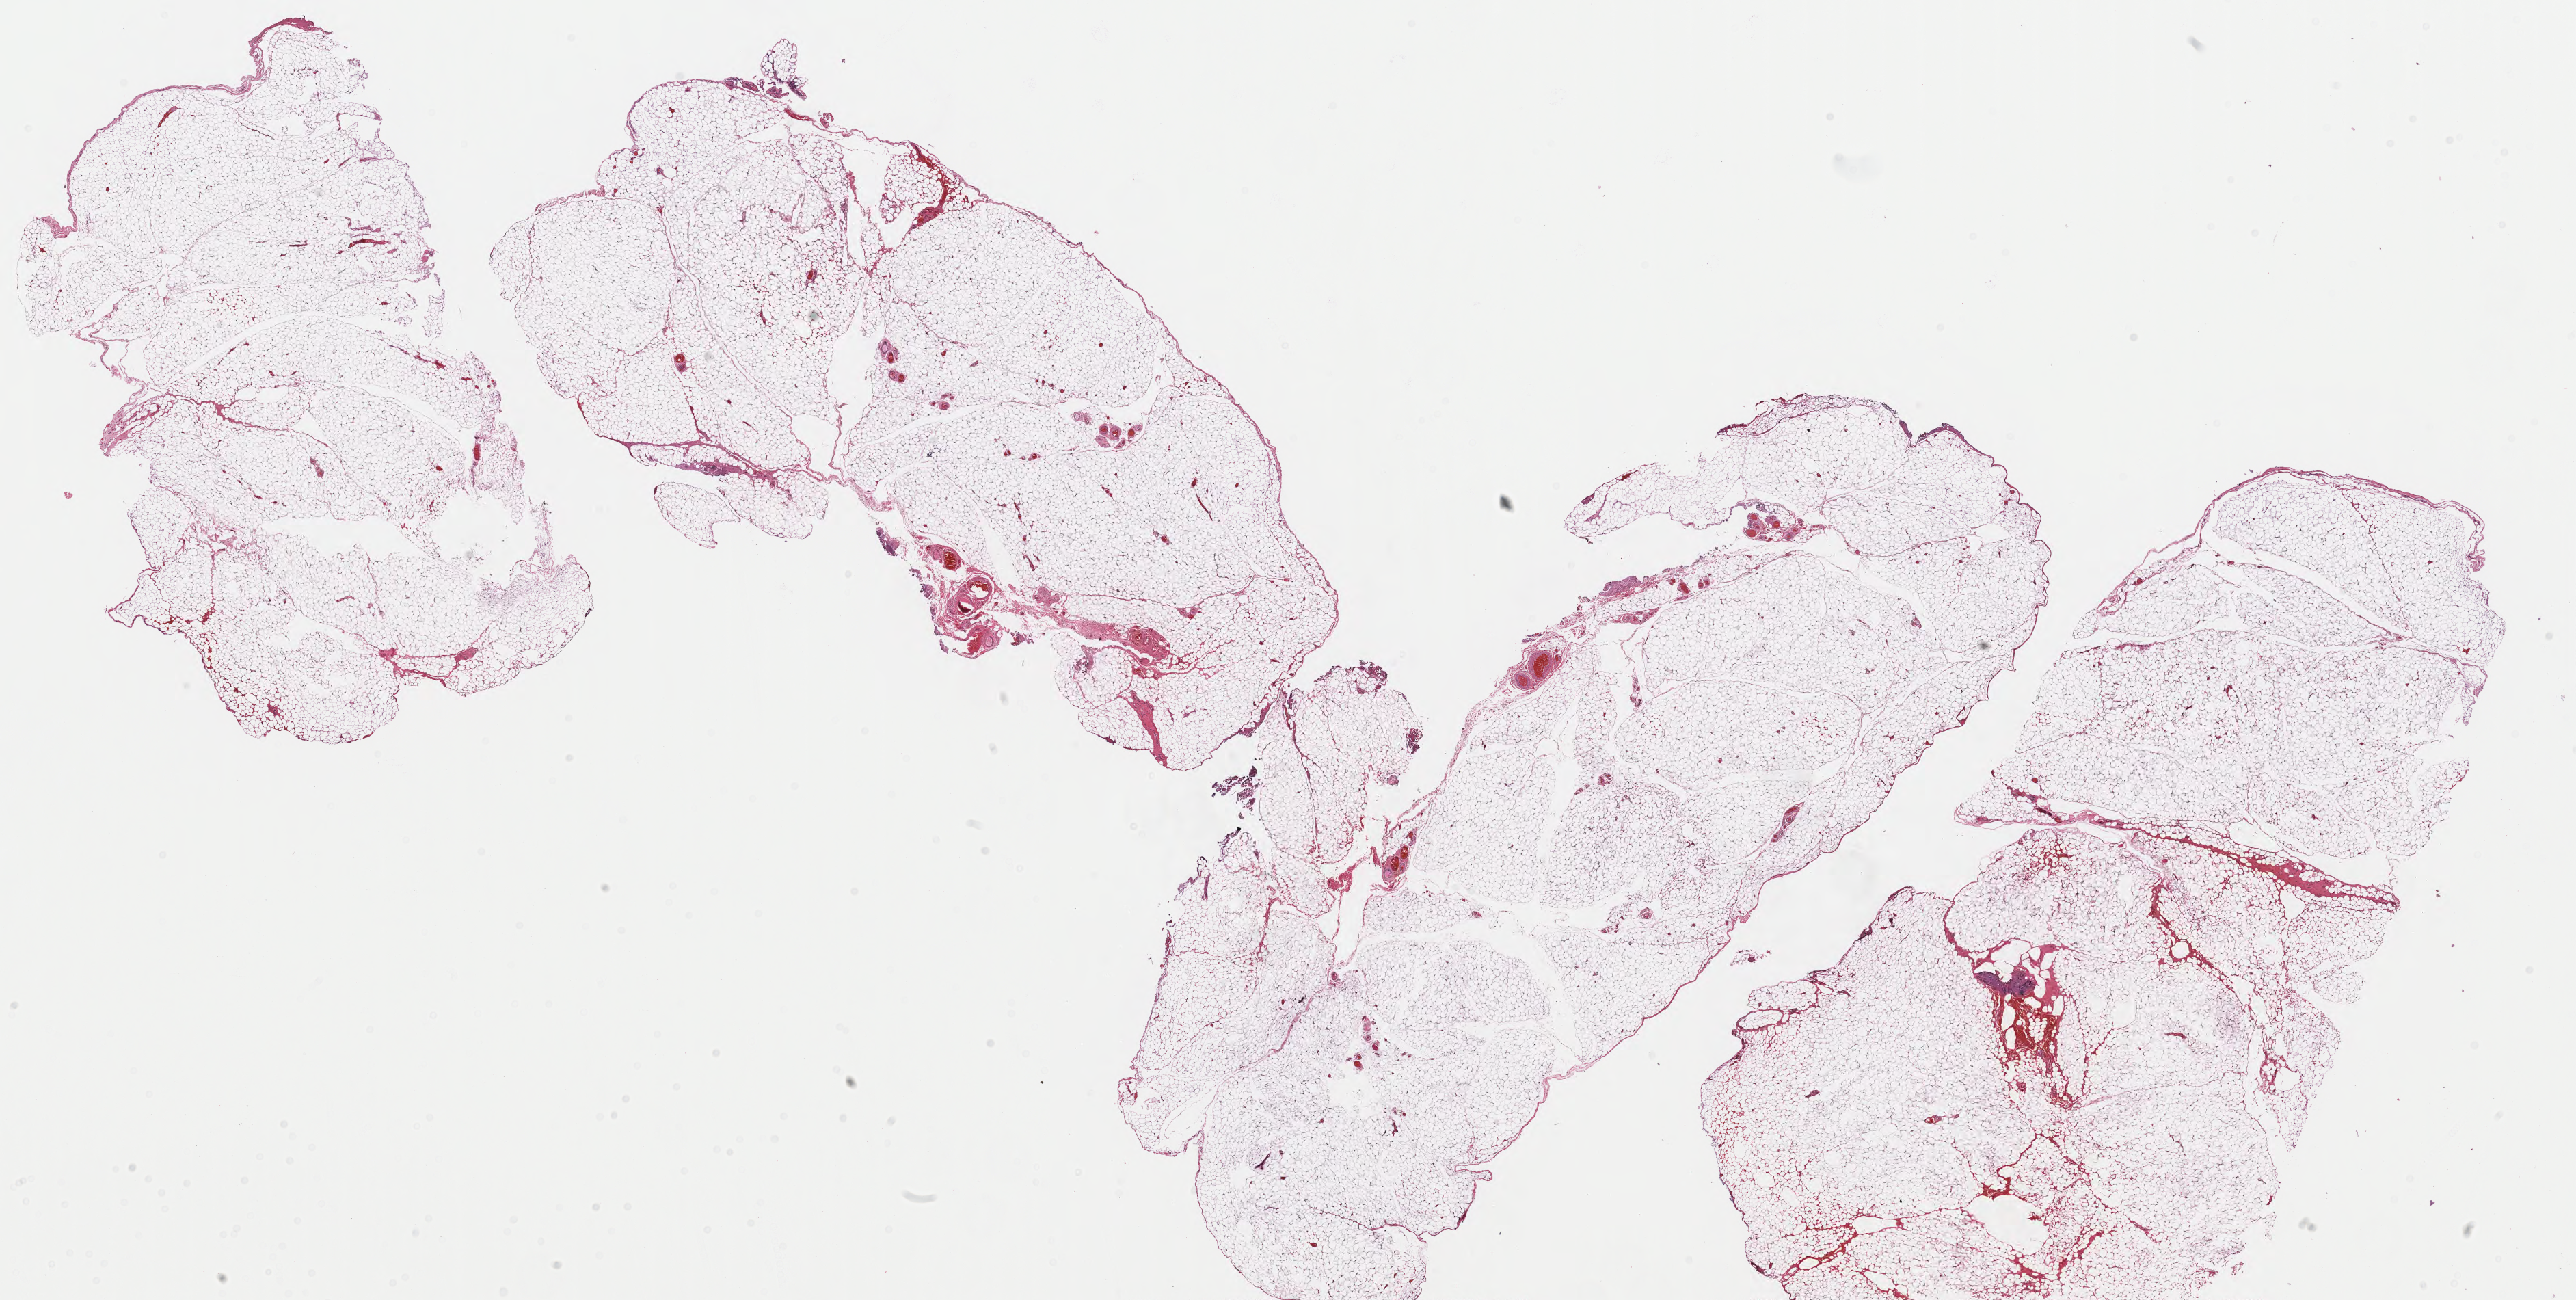
Whole-slide histology image, H&E-stained — low-resolution overview of the scanned area, about 29.9 x 15.1 mm (from a 40x scan); formalin-fixed paraffin-embedded (FFPE) diagnostic section; sample: primary tumour, thymus. Female patient; age at initial diagnosis 57 years.
- pathologic diagnosis: Thymoma, type B1, NOS